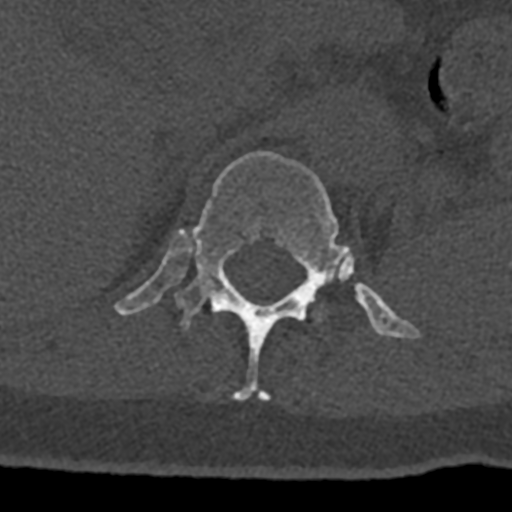
CT including the spine, one axial slice. Slice 493 of 797 in the series (ordered by position). 120 kVp. Bone window (W 1800 / L 400 HU). 0.5 mm slice thickness. 512 × 512 image matrix, field of view 160 × 160 mm. Male patient, age 74 years. Case-level facts recorded for this patient, not image findings: primary cancer: renal.
Annotated regions visible in this slice (semi-automatic segmentation, software-assisted and operator-edited):
- L1 vertebra: bounding box (x1, y1, x2, y2) in pixels: (313, 302, 322, 322)
- T12 vertebra: (114, 151, 420, 401)